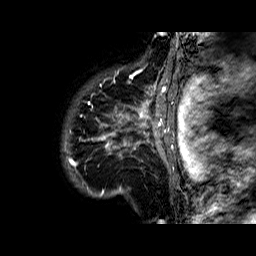
Breast MRI (dynamic contrast-enhanced), one sagittal slice; dynamic contrast-enhanced series, time point 2 of 6 at this slice position (early post-contrast); 1.5 T; TE 6.3 ms, TR 32.4 ms; 4 mm slice thickness; 256 × 256 image matrix. Female patient. From the clinical record (not read from this slice): setting: breast cancer imaged before/during neoadjuvant chemotherapy; receptor status: HR-positive, HER2-negative.
Outlined on this slice (semi-automatically segmented with operator editing):
- analysis volume of interest (the breast-tissue region the enhancement analysis was run in; not a lesion): bounding box (x1, y1, x2, y2) in pixels: (68, 72, 177, 183)
- tumour enhancement mask (voxels above the 100 % enhancement threshold inside the analysis volume of interest): (68, 72, 174, 168)